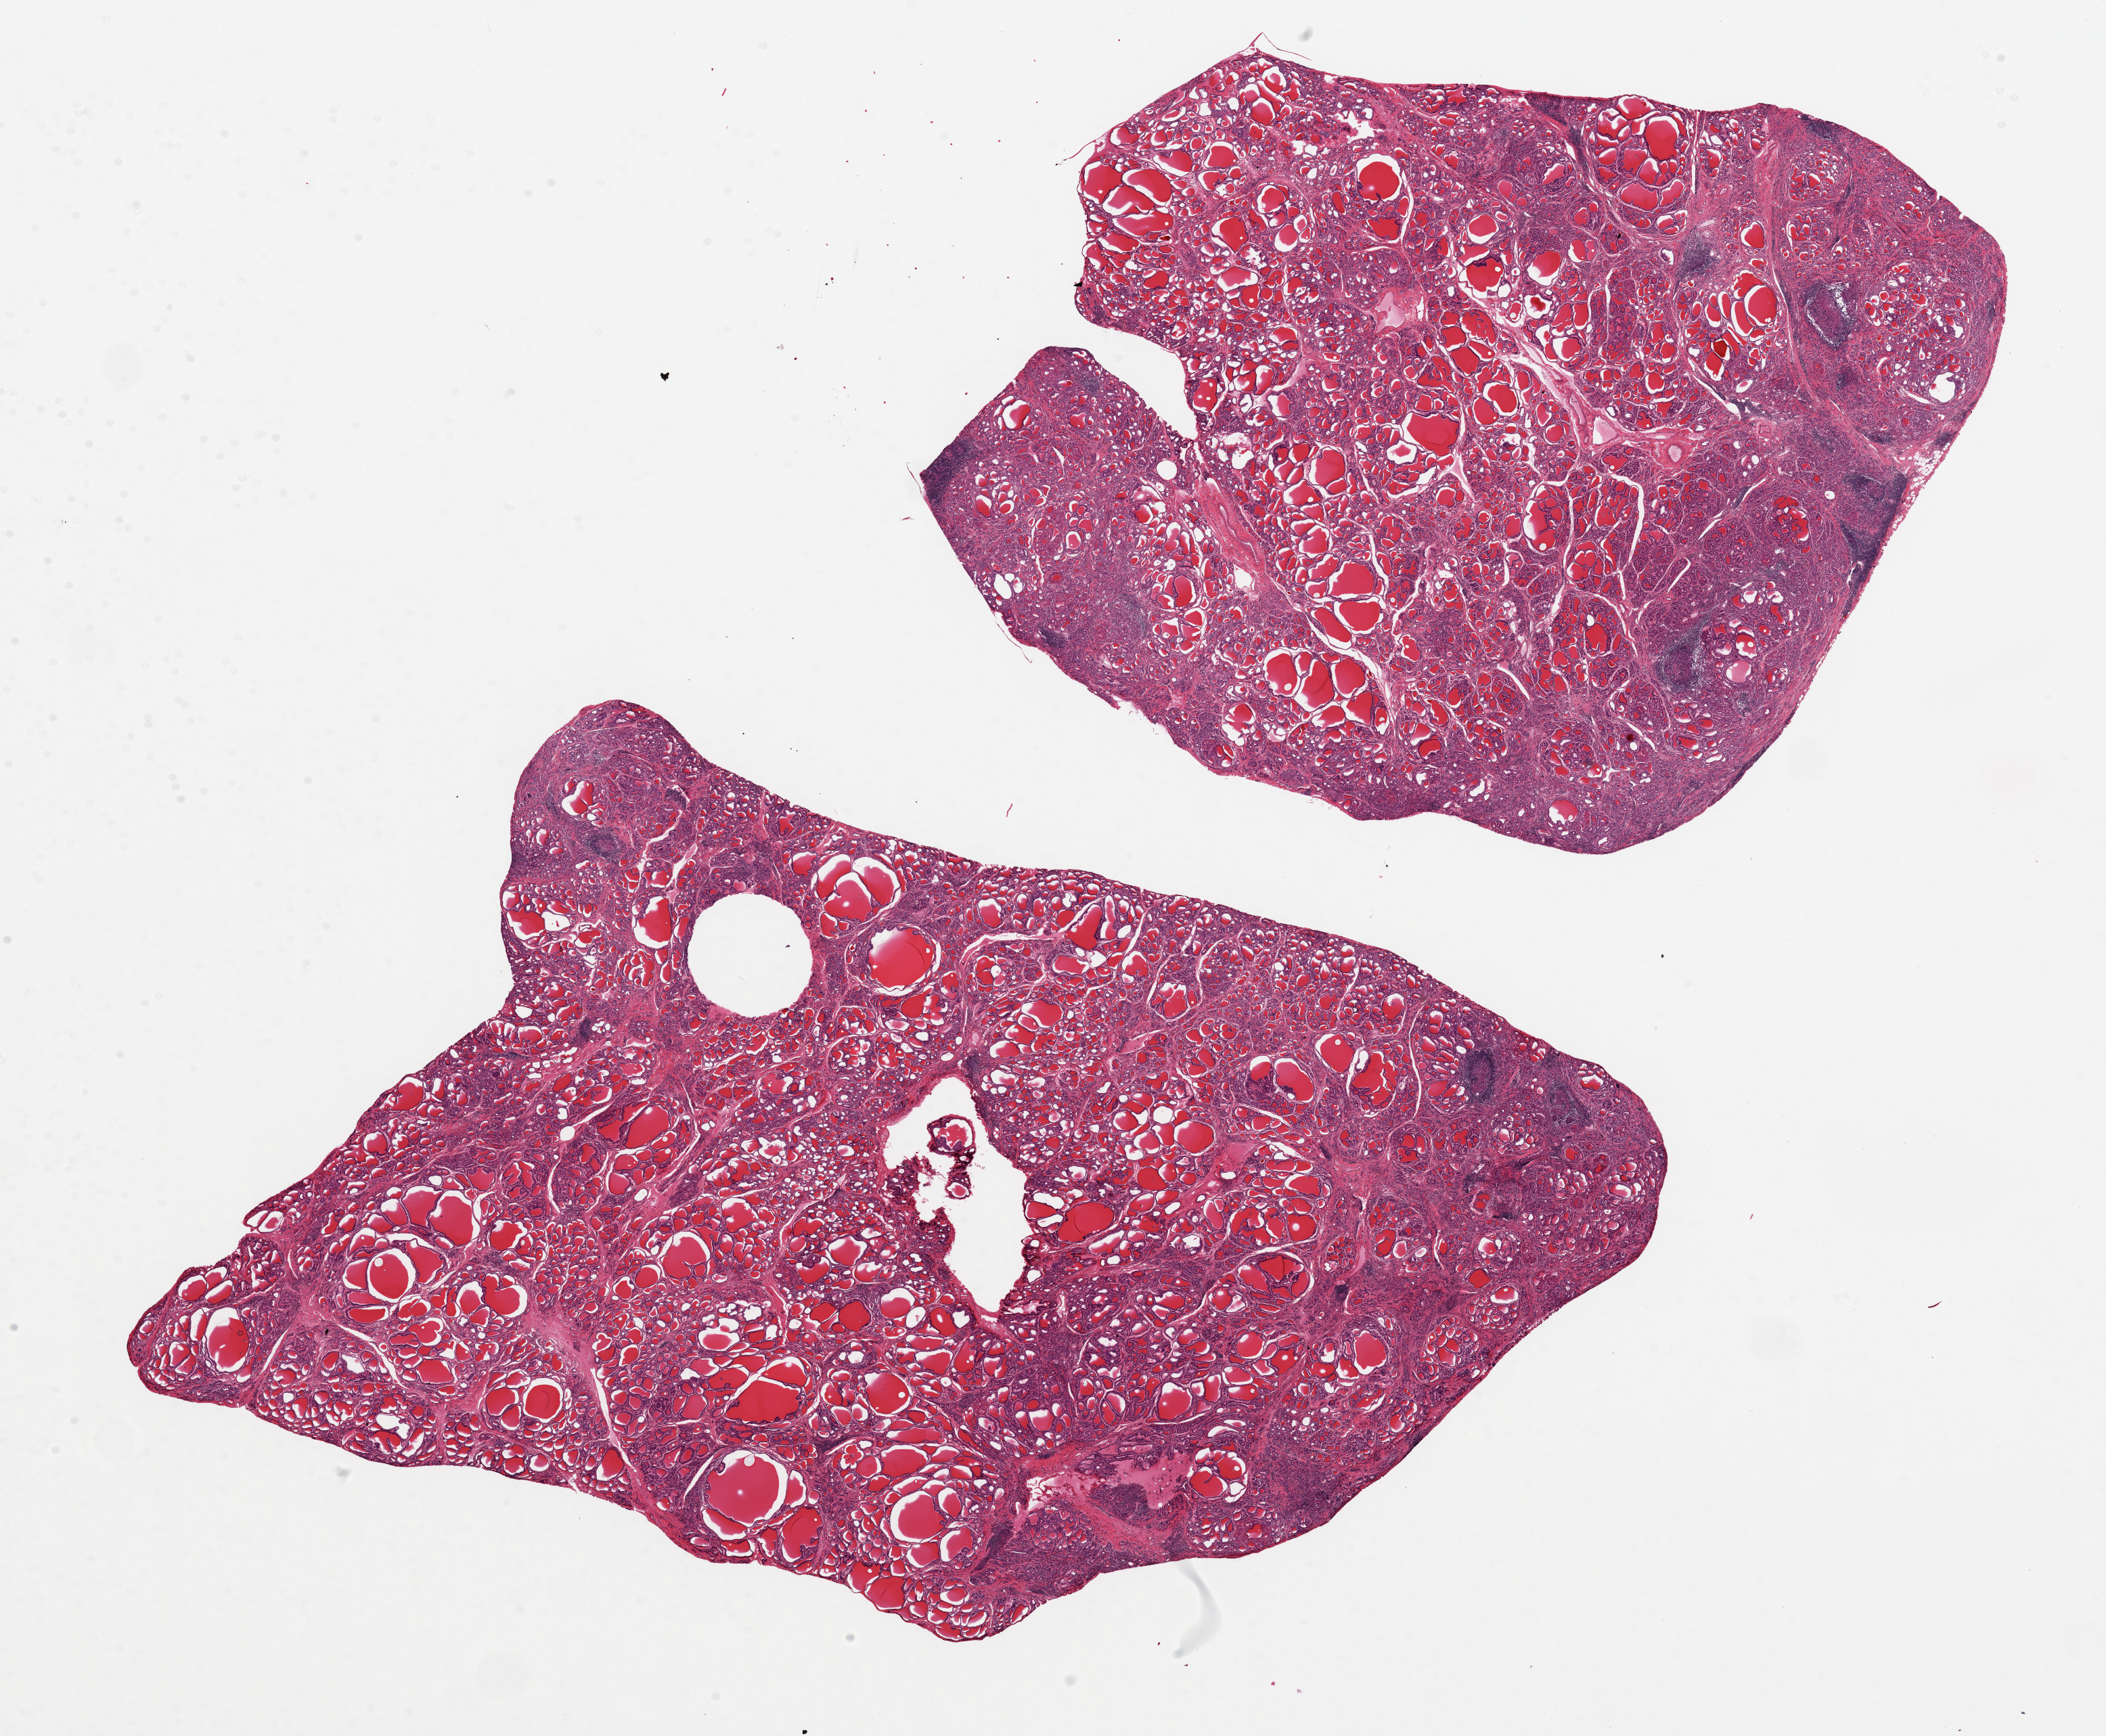
H&E whole-slide image, brightfield, shown as a low-resolution overview of the whole scanned area (about 24.6 x 20.3 mm, acquisition: 20x scan). PAXgene-fixed, paraffin-embedded tissue. Target tissue: thyroid. Tissue donor sample. Male donor.
* review note (as recorded): 2 aliquots, ~12x8mm; Diffuse Hashimoto's/lymphocytic thyroiditis; Germinal centers